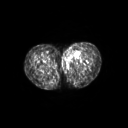
FDG PET of an extremity soft-tissue mass (from a PET/CT study), one axial slice. Slice 43 of 267 in the series (ordered by position). 128 × 128 image matrix, field of view 600 × 600 mm. Patient: female, 24 years. From the clinical record (not read from this slice): histological type: leiomyosarcoma; grade: high; site of the primary tumour: groin.
Outlined on this slice (expert contour drawn on MRI and transferred to this co-registered scan by the dataset authors):
- gross tumour volume including surrounding oedema: bounding box (x1, y1, x2, y2) in pixels: (61, 48, 80, 64)